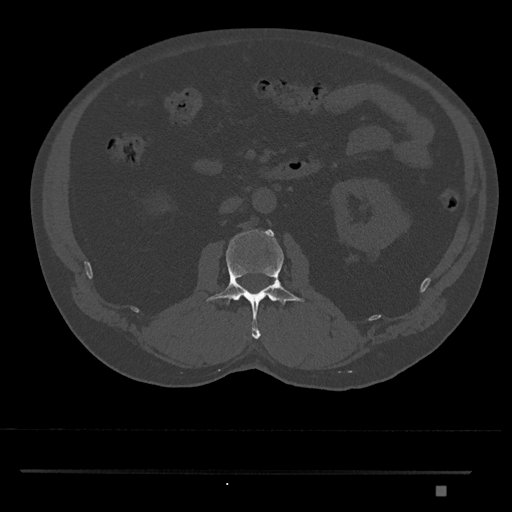
CT including the spine, one axial slice; slice 751 of 1134 in the series (ordered by position); reconstruction kernel Br40s/3; 120 kVp; bone window (W 1800 / L 400 HU); 0.5 mm slice thickness; 512 × 512 image matrix, field of view 429 × 429 mm. Patient: male, 65 years. Case-level facts recorded for this patient, not image findings: primary cancer: prostate.
Annotated regions visible in this slice (semi-automatically segmented with operator editing):
- L2 vertebra: bounding box <206,229,305,339> (left, top, right, bottom; pixels)